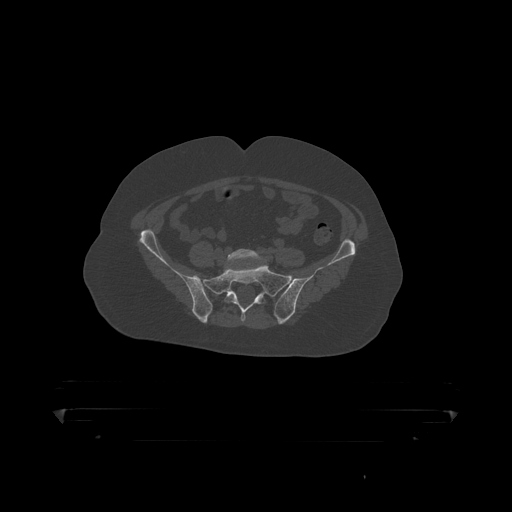
CT including the spine, one axial slice; position 21 of 390 along the scan axis; reconstruction kernel STANDARD; 120 kVp; bone window (W 1800 / L 400 HU); 512 × 512 image matrix, field of view 650 × 650 mm. Male patient, age 60 years. Case-level facts recorded for this patient, not image findings: primary cancer: prostate.
Annotated regions visible in this slice (semi-automatically segmented with operator editing):
- L5 vertebra: bounding box <224,249,263,266> (left, top, right, bottom; pixels)